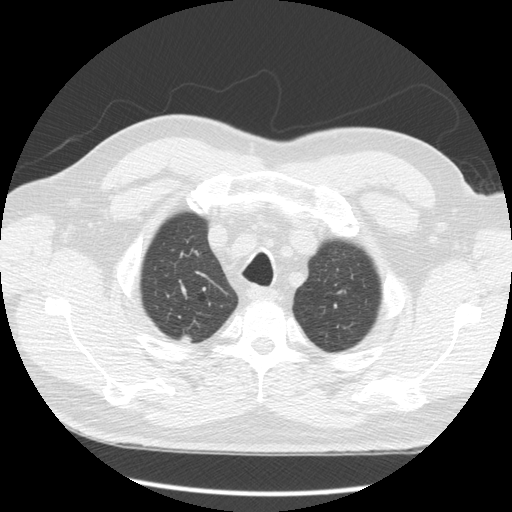
Low-dose screening chest CT, one axial slice; position 146 of 163 along the scan axis; lung window (W 1500 / L -600 HU); 2.5 mm slice thickness; 512 × 512 image matrix, field of view 360 × 360 mm.
Outlined on this slice (outlined manually by an expert reader):
- lesion 1 (tumor, upper lobe of right lung): bounding box <181,335,192,345> (left, top, right, bottom; pixels)